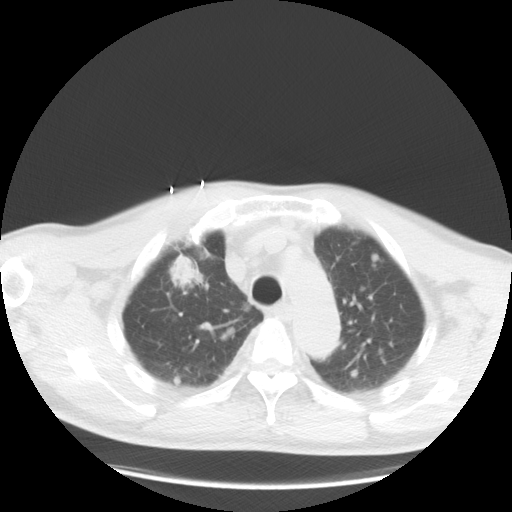
Chest CT, one axial slice. Position 24 of 36 along the scan axis. Reconstruction kernel STANDARD. 120 kVp. Lung window (W 1500 / L -600 HU). 5 mm slice thickness. 512 × 512 image matrix, field of view 369 × 369 mm. Patient: male, 57 years. Case-level facts recorded for this patient, not image findings: clinical TNM (as recorded): T2 N3 M1a.
Annotated regions visible in this slice (rectangle marked by the reading radiologist):
- lung tumour (recorded histology: adenocarcinoma): bounding box [x1, y1, x2, y2] px = [167, 251, 202, 288]